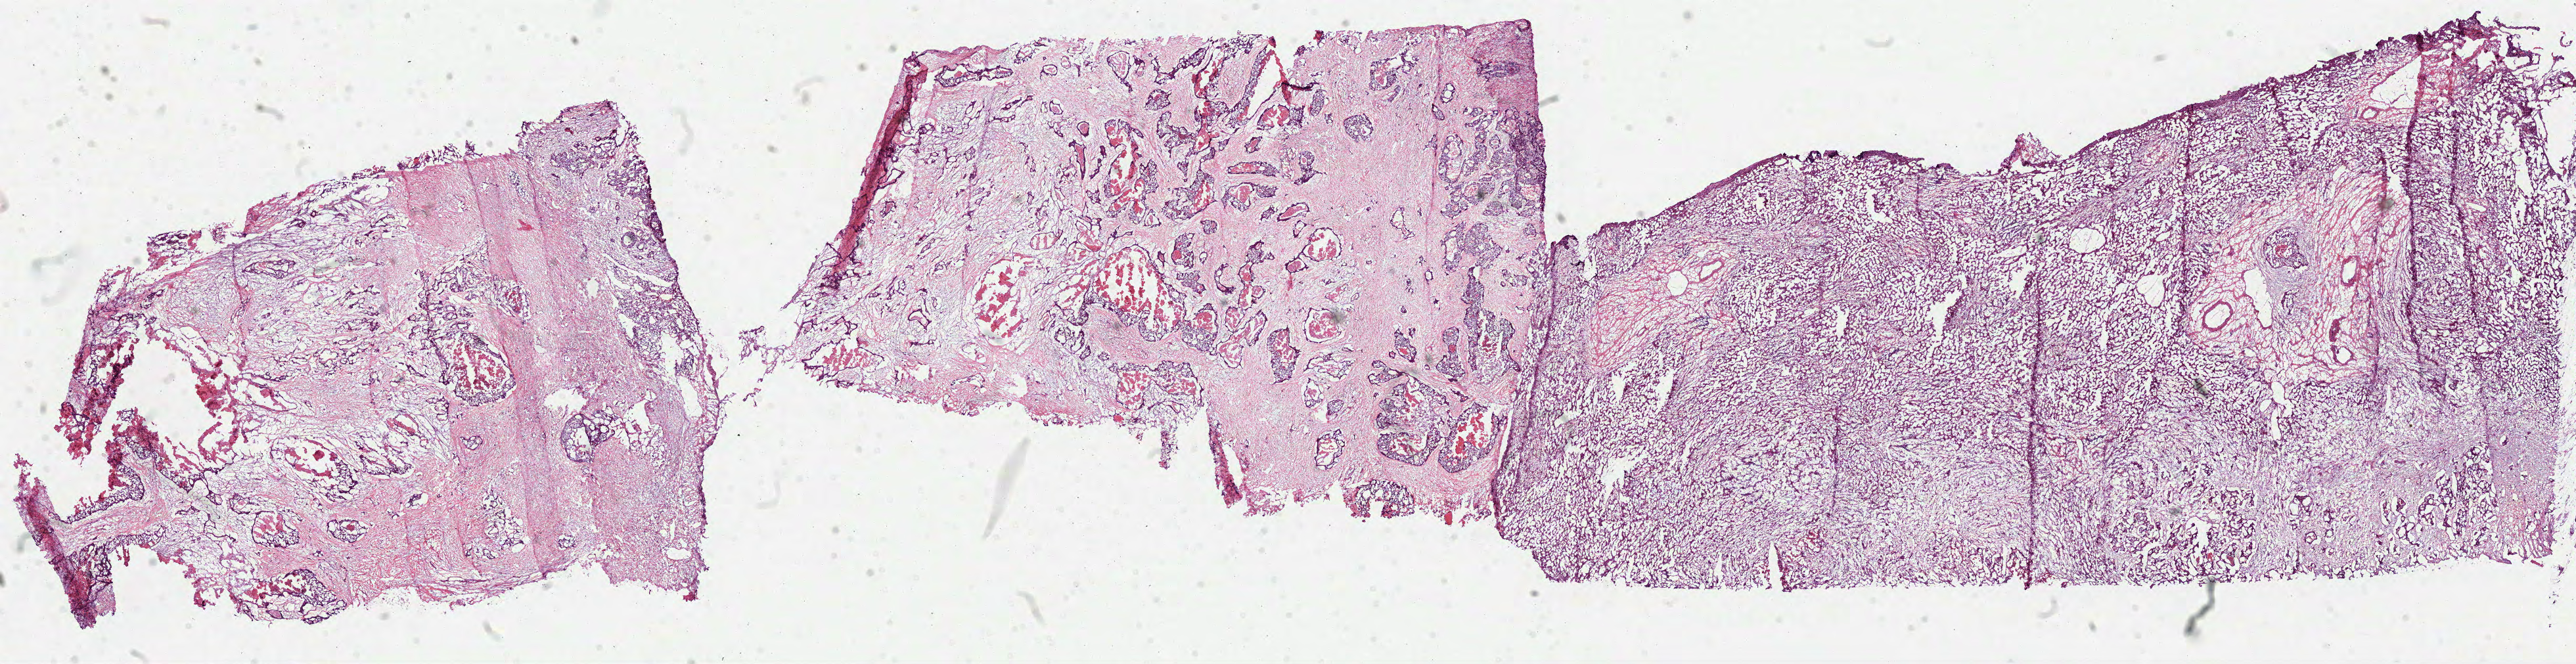
H&E whole-slide image — shown as a low-resolution overview of the whole scanned area (about 31.6 x 8.2 mm, from a 40x scan). Frozen section. Recurrent tumour sample from the rectum. Patient: male, age at initial diagnosis 56 years. Pathologist review of this section (percent, as recorded): tumour cells 70%, tumour nuclei 85%, normal cells 0%, stromal cells 20%, necrosis 10%.
This section: recurrent tumour. Patient diagnosis: Adenocarcinoma, NOS (rectosigmoid junction).